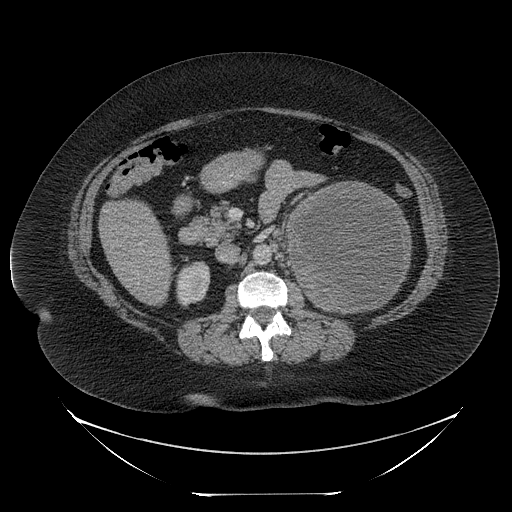
Contrast-enhanced abdominal CT, one axial slice. Slice 128 of 205 in the series (ordered by position). Reconstruction kernel STANDARD. 120 kVp. Intravenous contrast given. Soft-tissue window (W 400 / L 40 HU). 2.5 mm slice thickness. 512 × 512 image matrix. Patient: female, 53 years. From the clinical record (not read from this slice): diagnosis: adrenocortical carcinoma; tumour side: left adrenal; tumour size at pathology: 17 cm; Ki-67 index: 20 %; stage (as recorded): 3.
Structures marked on this image (semi-automatic segmentation, software-assisted and operator-edited):
- mass: bounding box [x1, y1, x2, y2] px = [289, 183, 410, 311]